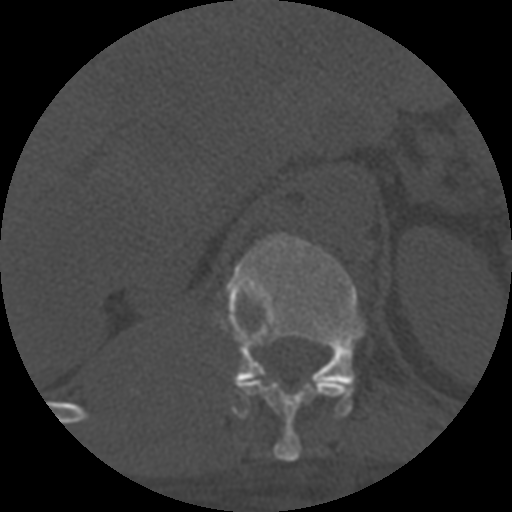
CT including the spine, one axial slice; slice 323 of 708 in the series (ordered by position); reconstruction kernel STANDARD; 120 kVp; one of 3 acquisitions stored at this slice position; bone window (W 1800 / L 400 HU); 1.25 mm slice thickness; 512 × 512 image matrix, field of view 160 × 160 mm. Patient age 55 years. From the clinical record (not read from this slice): primary cancer: colon.
Outlined on this slice (semi-automatically segmented with operator editing):
- T11 vertebra: box from (x=235, y=379) to (x=348, y=462) px
- T12 vertebra: (x=226, y=234)–(x=364, y=418)